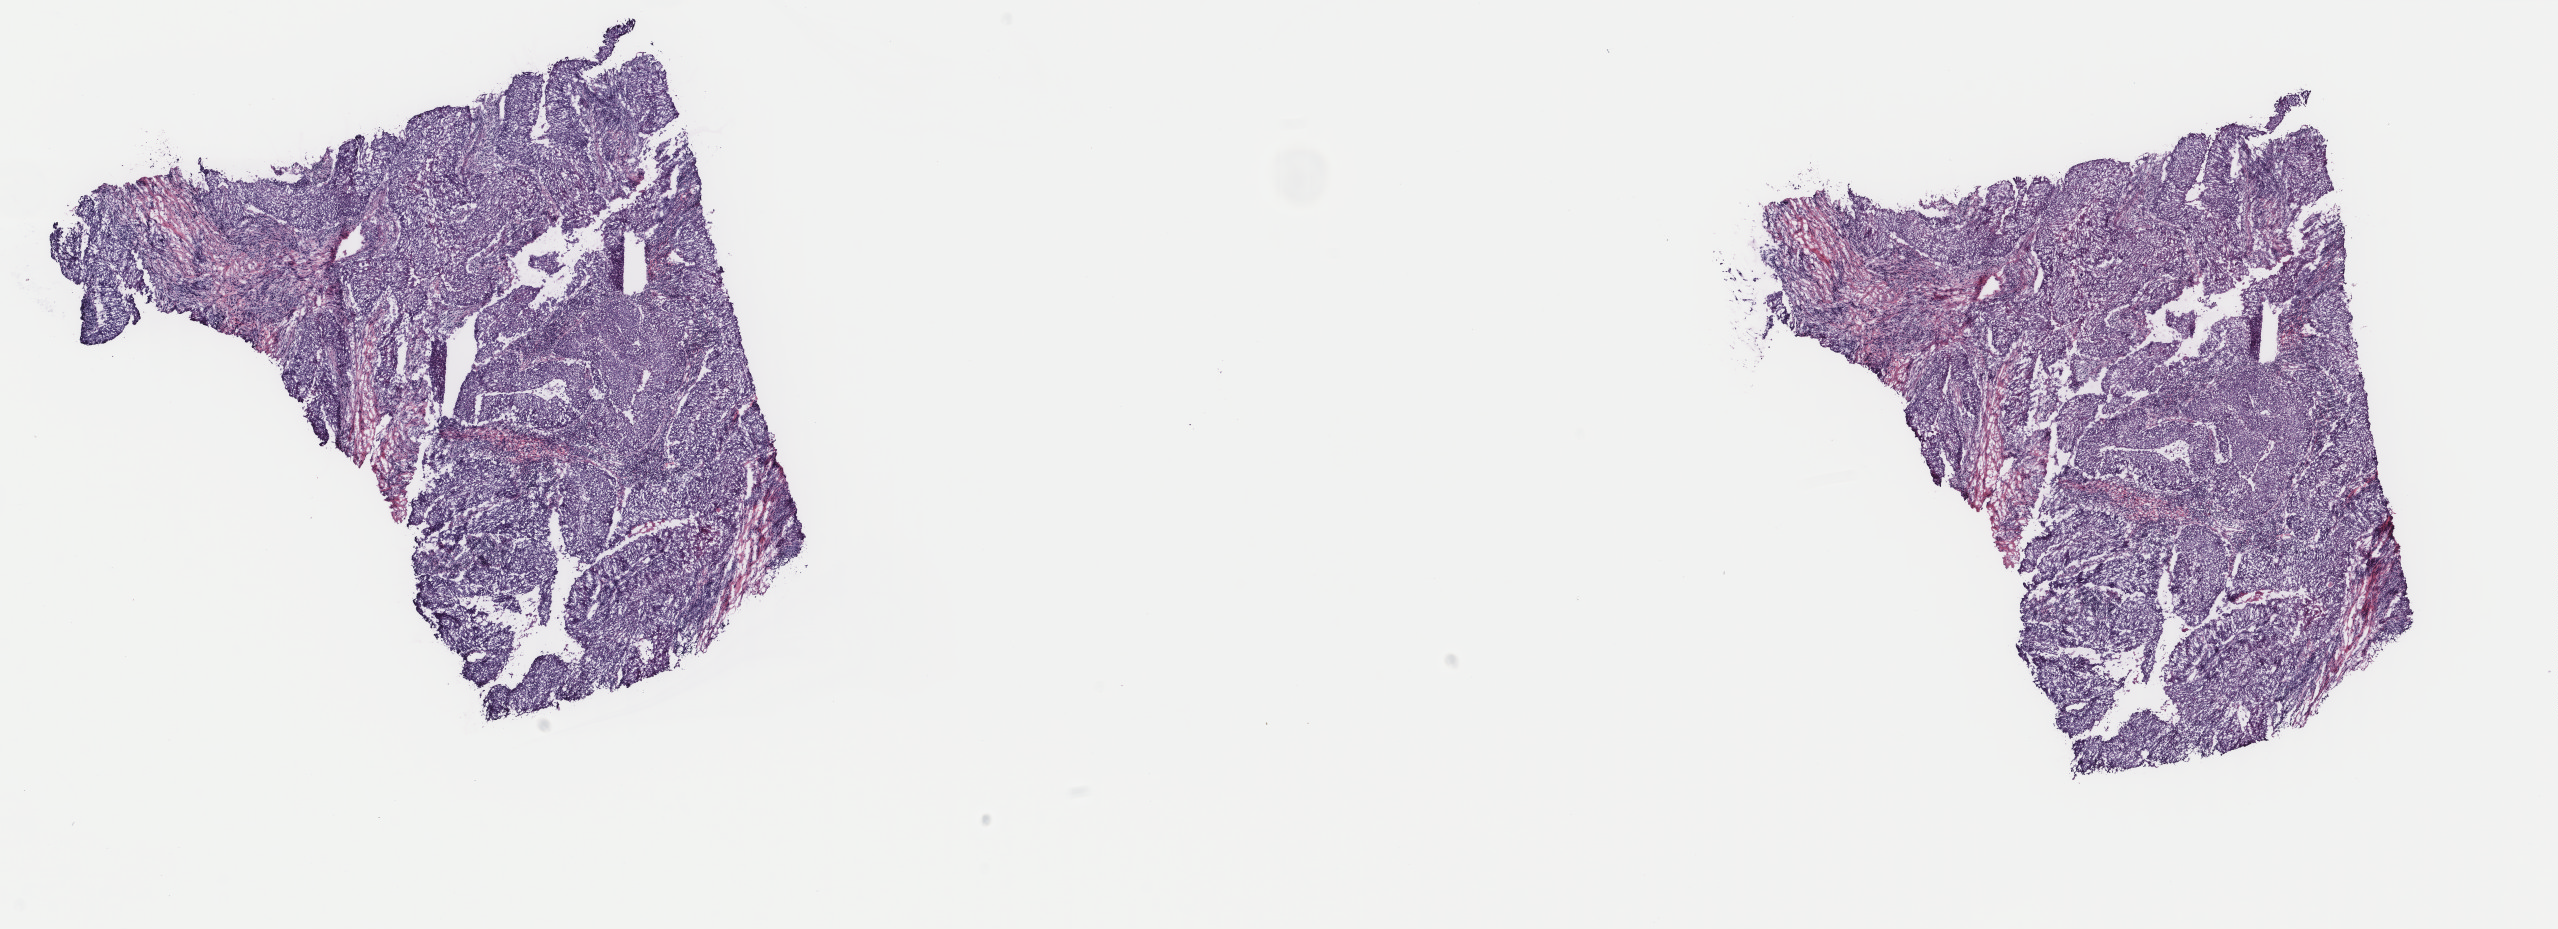
Digitized Hematoxylin and eosin (H&E) stained tissue section (whole slide), shown as a low-resolution overview of the whole scanned area (about 20.3 x 7.4 mm, slide scanned at 40x). Frozen section from the top of the tissue portion. Head and neck, primary tumour sample. Male patient; age at initial diagnosis 49 years. Histologic grade: G2 (moderately differentiated). Slide review estimates, as recorded: tumour cells 100%, tumour nuclei 75%, normal cells 0%, stromal cells 0%, necrosis 0%. Infiltration values recorded for this section: lymphocyte infiltration 8%, monocyte infiltration 0%, neutrophil infiltration 1%.
* pathologic diagnosis: Squamous cell carcinoma, NOS (tonsil, NOS)